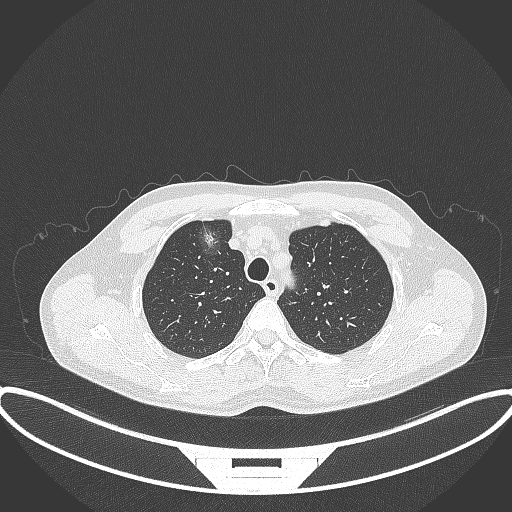
Chest CT, one axial slice; slice 293 of 395 in the series (ordered by position); reconstruction kernel B70f; 120 kVp; lung window (W 1500 / L -600 HU); 1 mm slice thickness; 512 × 512 image matrix, field of view 424 × 424 mm. Patient: male, 60 years. From the clinical record (not read from this slice): clinical TNM (as recorded): T1c N0 M0.
Annotated regions visible in this slice (rectangle marked by the reading radiologist):
- lung tumour (recorded histology: adenocarcinoma): bounding box [x1, y1, x2, y2] px = [191, 214, 229, 264]